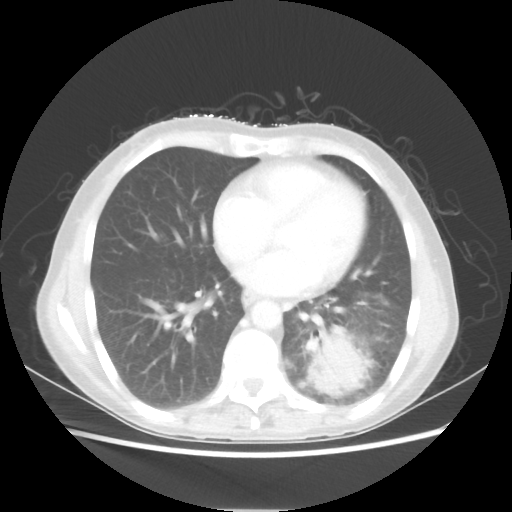
Chest CT, one axial slice. Position 23 of 56 along the scan axis. 80 kVp. Lung window (W 1500 / L -600 HU). 5 mm slice thickness. 512 × 512 image matrix, field of view 360 × 360 mm. Female patient, age 53 years. From the clinical record (not read from this slice): clinical TNM (as recorded): T3 N0 M0.
Structures marked on this image (rectangle marked by the reading radiologist):
- lung tumour (recorded histology: adenocarcinoma): bounding box (x1, y1, x2, y2) in pixels: (305, 329, 372, 396)